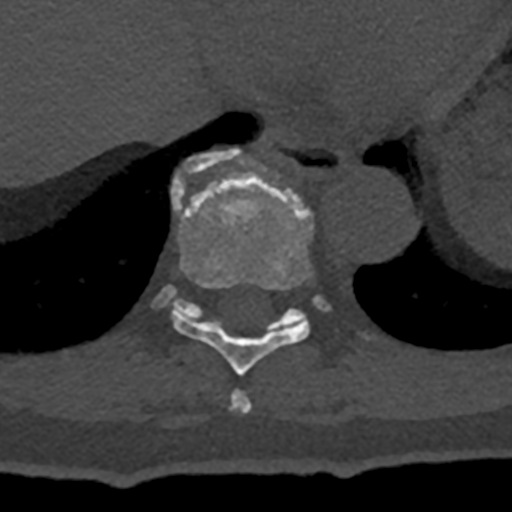
CT including the spine, one axial slice; position 641 of 797 along the scan axis; 120 kVp; bone window (W 1800 / L 400 HU); 512 × 512 image matrix. Male patient, age 74 years. From the clinical record (not read from this slice): primary cancer: renal; vertebrae with lytic lesions (as recorded): T10, L1, L2, L3, L4, L5.
Structures marked on this image (semi-automatically segmented with operator editing):
- T10 vertebra: box from (x=153, y=149) to (x=373, y=340) px
- T8 vertebra: (x=231, y=390)–(x=252, y=414)
- T9 vertebra: (x=172, y=176)–(x=314, y=375)